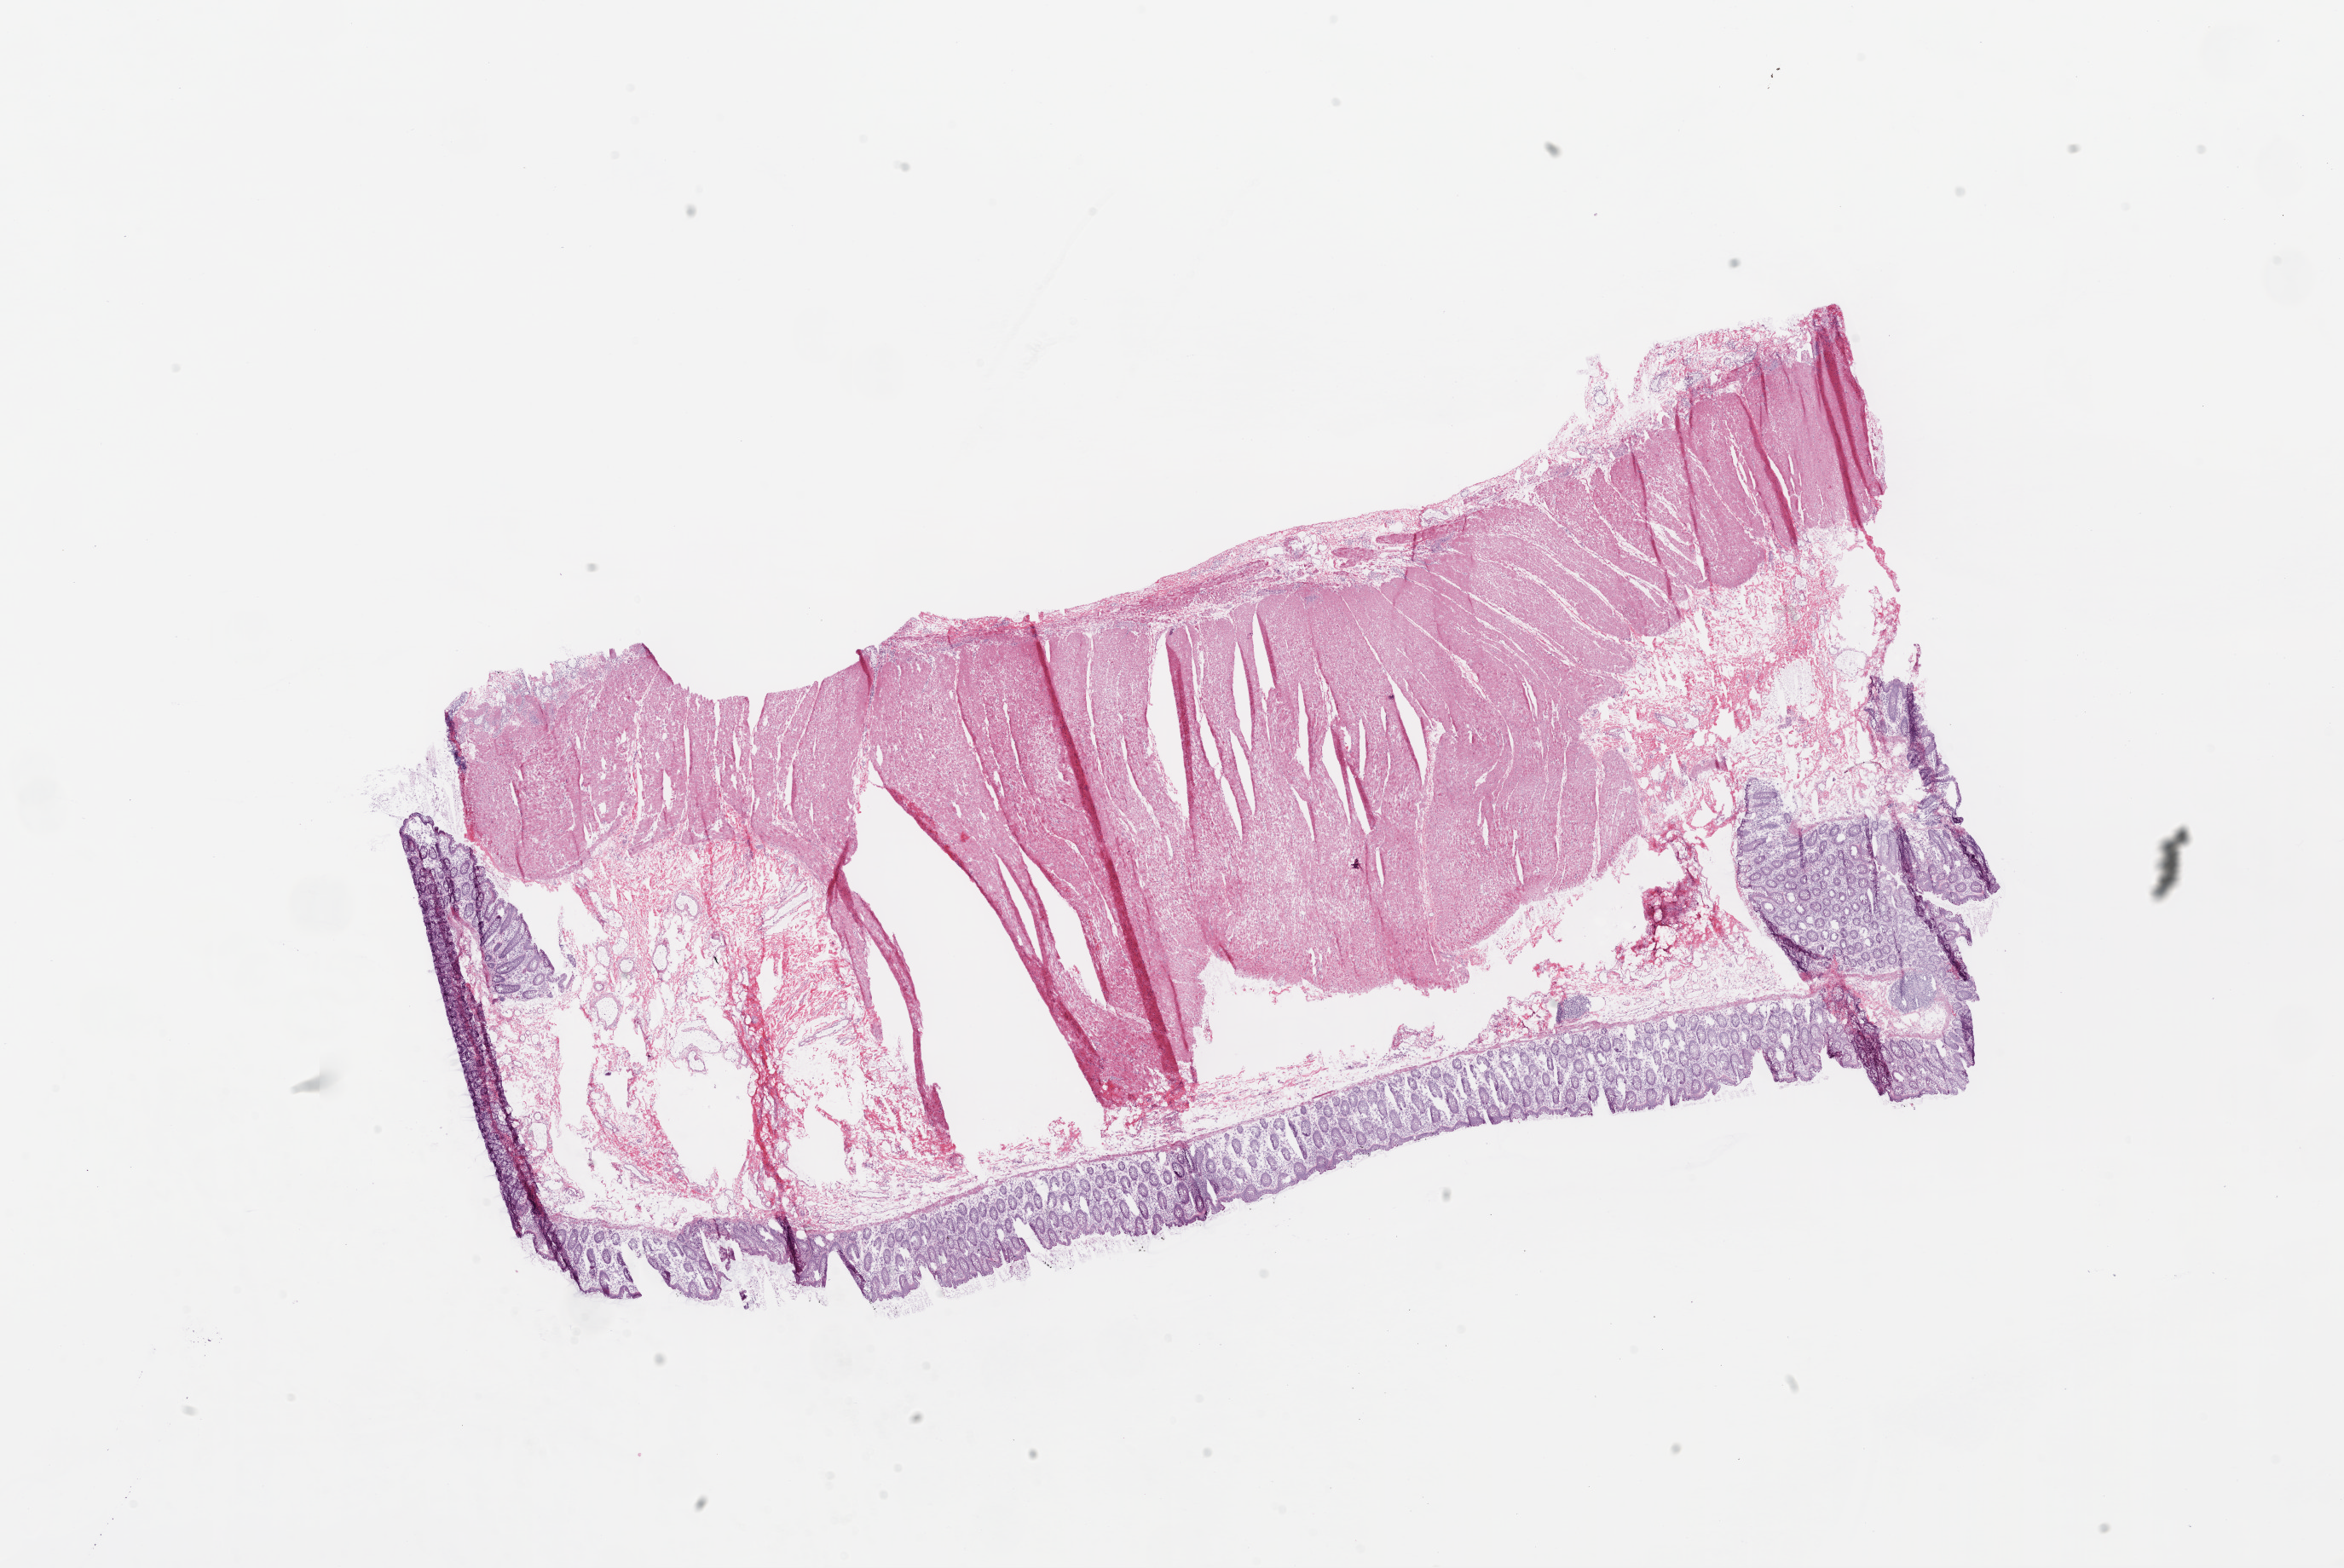
Whole-slide histology image, H&E-stained, low-resolution overview of the scanned area, about 22.1 x 14.8 mm. Frozen section from the bottom of the tissue portion. Sample: solid tissue normal (non-tumour tissue), colon. Male patient; age at initial diagnosis 62 years.
This section: solid tissue normal sample (biorepository sample class). Patient diagnosis: Adenocarcinoma, NOS.